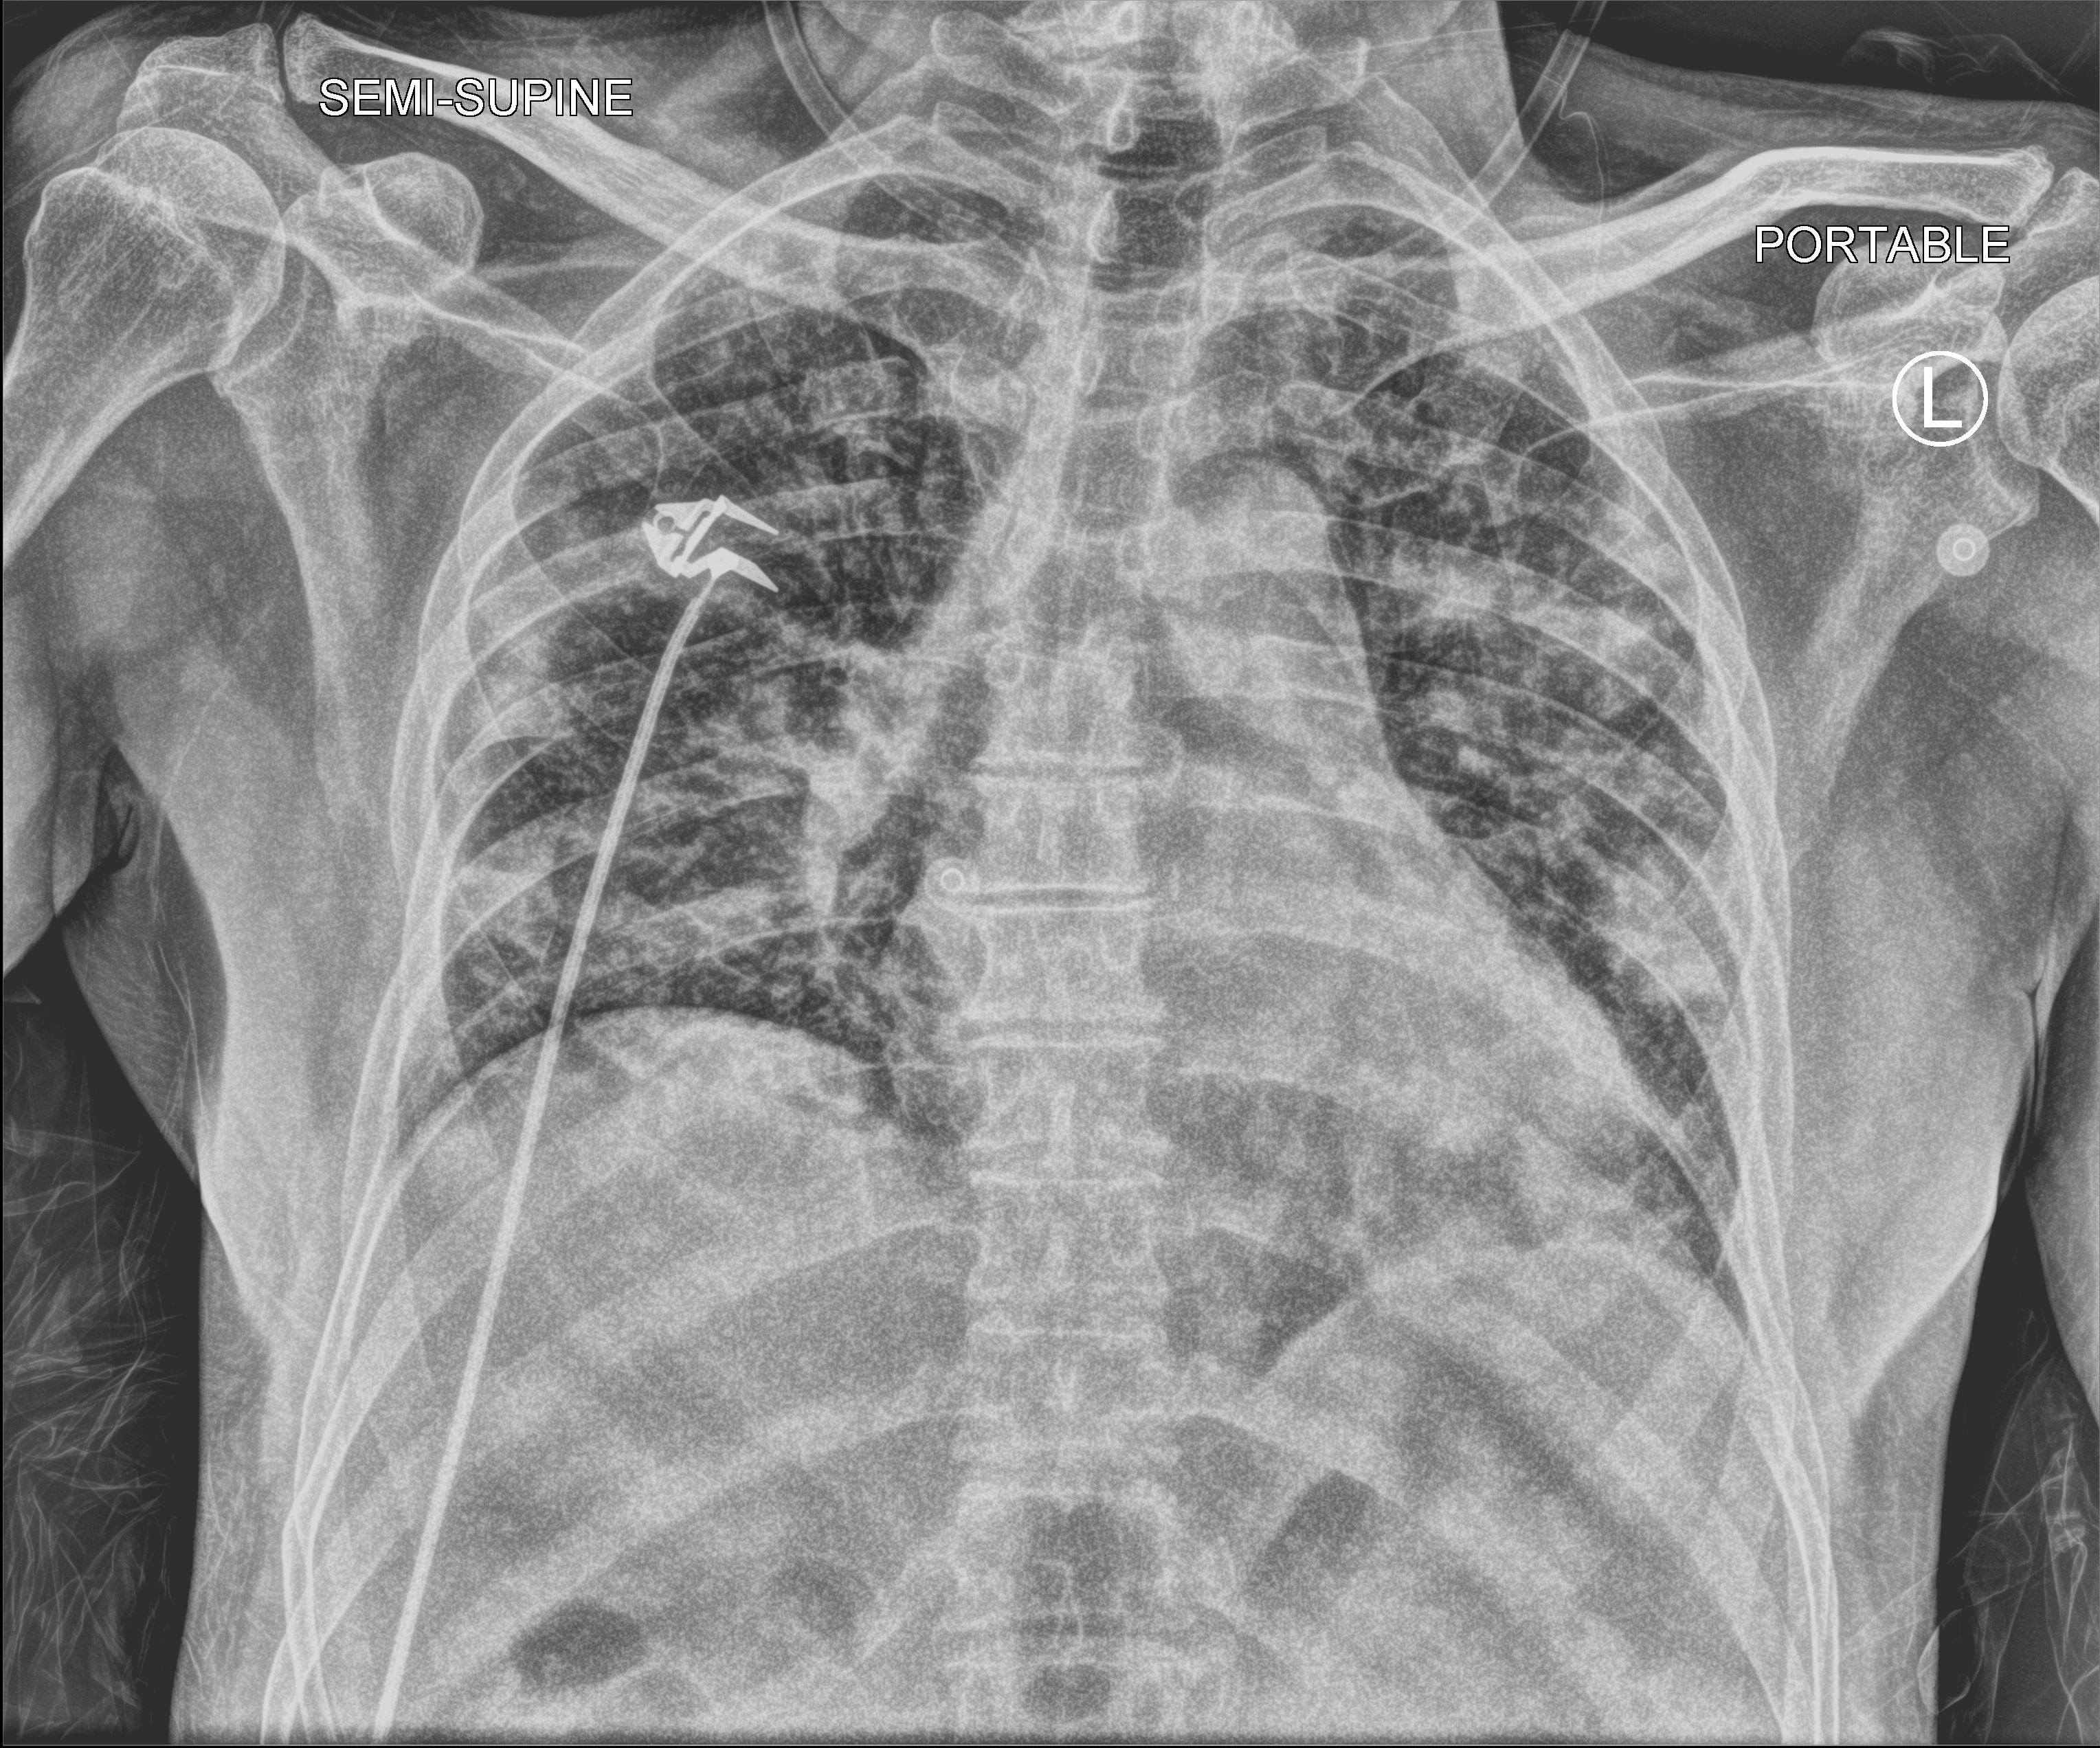
Chest X-ray (portable), anteroposterior (AP) projection. Male patient hospitalised with COVID-19, age 60–74 years.
Hospital-stay facts (about this admission, not read from this image; timing relative to this image not recorded):
- mechanically ventilated during this hospital stay: no
- admitted to intensive care during this hospital stay: no